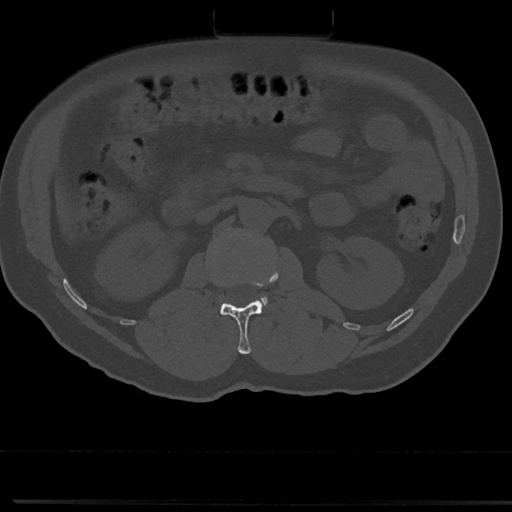
CT including the spine, one axial slice; slice 55 of 817 in the series (ordered by position); 120 kVp; bone window (W 1800 / L 400 HU); 0.5 mm slice thickness; 512 × 512 image matrix, field of view 355 × 355 mm. Male patient, age 61 years. Case-level facts recorded for this patient, not image findings: primary cancer: prostate.
Structures marked on this image (semi-automatically segmented with operator editing):
- L1 vertebra: bounding box [x1, y1, x2, y2] px = [220, 265, 278, 354]
- L2 vertebra: [215, 230, 269, 311]